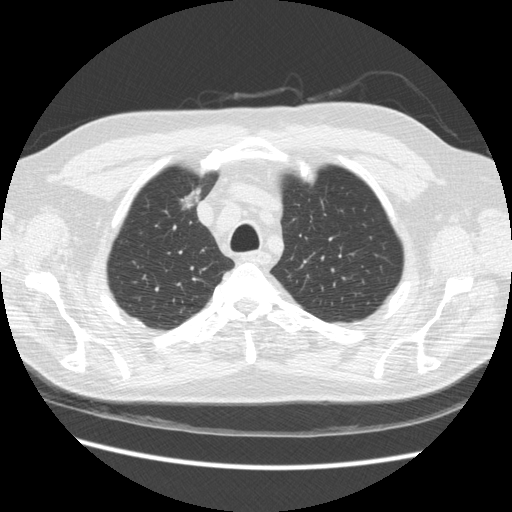
Chest CT (low-dose screening protocol), one axial image, third screening round (two years after baseline), lung window (W 1500 / L -600 HU), 2.5 mm slice thickness, slice 48 of 234 in the series. Male participant, aged 66 years at enrolment. Former smoker at enrolment.
• Expert reader's lesion annotation, bounding box [x1, y1, x2, y2] px = [166, 179, 212, 220].
• No non-calcified nodule or mass ≥4 mm was recorded by the screening reader at this exam.
• Official screen result: positive, other.